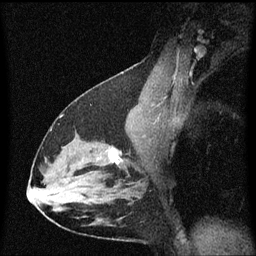
Breast MRI (dynamic contrast-enhanced), one sagittal slice. Position 36 of 60 along the scan axis. Dynamic contrast-enhanced series, image 2 of 3 at this slice position (ordered by acquisition). 1.5 T. TE 4.2 ms, TR 8.4 ms. 256 × 256 image matrix, field of view 200 × 200 mm. Patient: female, 38 years. From the clinical record (not read from this slice): setting: breast cancer imaged before/during neoadjuvant chemotherapy; receptor status: HR-positive, HER2-negative.
Structures marked on this image (semi-automatically segmented with operator editing):
- analysis volume of interest (the breast-tissue region the enhancement analysis was run in; not a lesion): bounding box (x1, y1, x2, y2) in pixels: (94, 138, 141, 185)
- tumour enhancement mask (voxels above the 70 % enhancement threshold inside the analysis volume of interest): (110, 150, 123, 165)